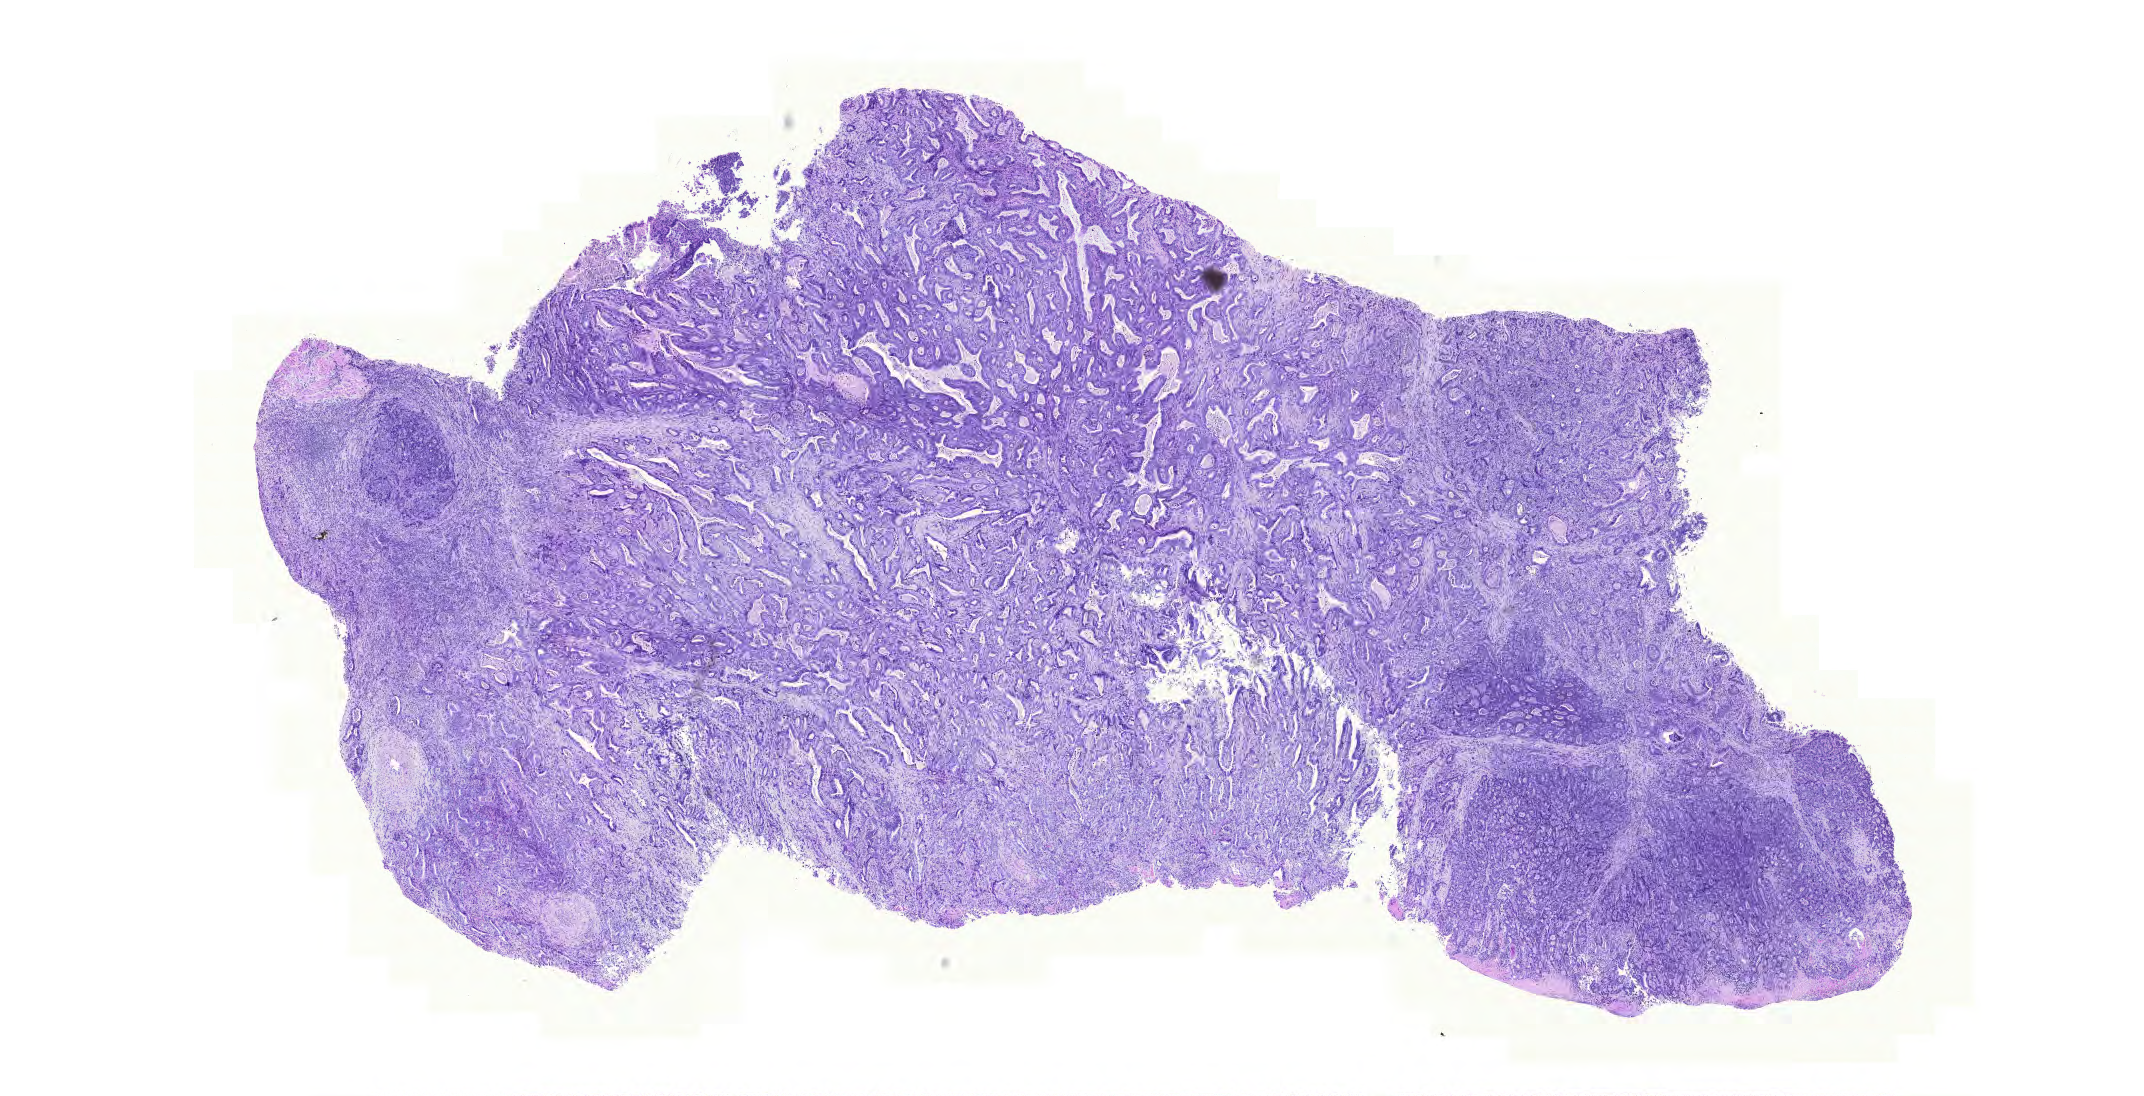
Hematoxylin and eosin (H&E) stained whole-slide image — a low-resolution overview of the entire scanned area, about 16.0 x 8.2 mm (acquisition: 20x scan); FFPE section; primary tumour sample from the stomach. Female patient; age at initial diagnosis 58 years. Histologic grade: G3 (poorly differentiated).
Diagnosis: Adenocarcinoma, intestinal type (cardia, NOS). Lymph nodes positive (case pathology): 0 of 17 examined. AJCC pathologic stage: IB (6th edition). TNM: T2a N0 M0.